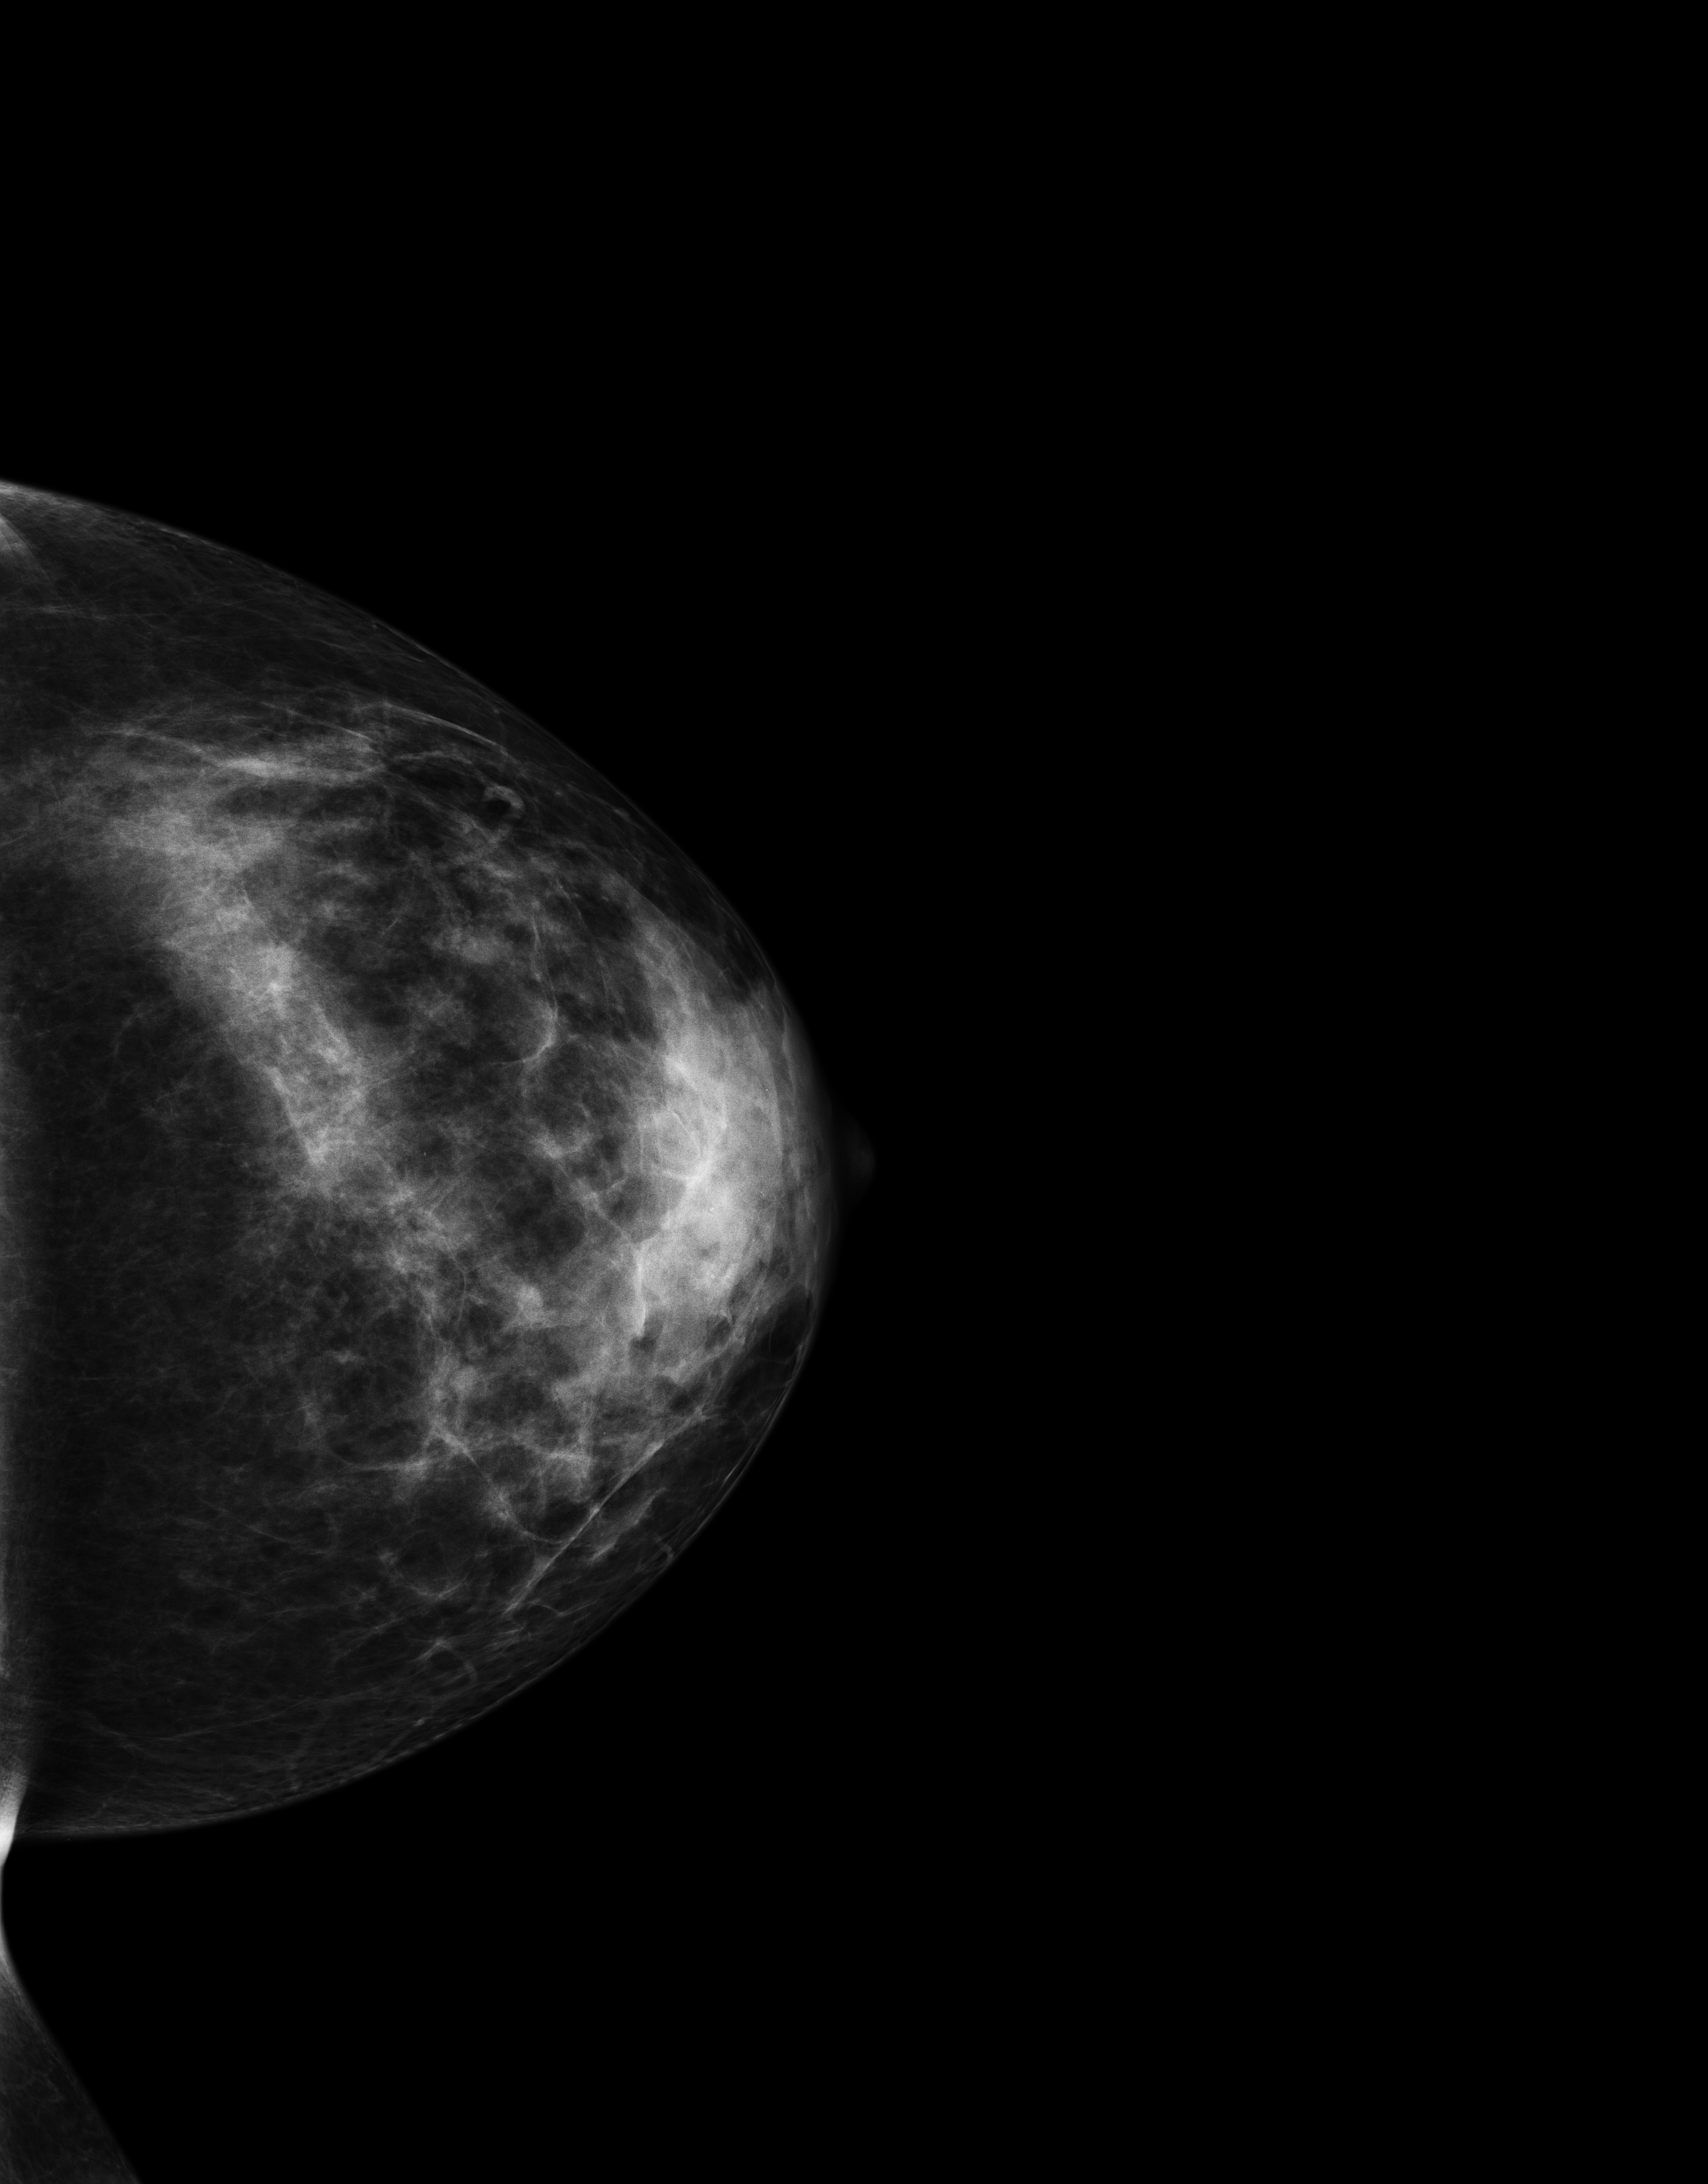
Digital mammogram (FFDM), left breast, CC view, annual screening mammography examination. Patient aged 46 years (female).
- BI-RADS breast density category at the screening exam (both breasts, scale 1–4): 3
- final BI-RADS category for the screening round (tomosynthesis exam, both breasts): category 1
- recall: no recall after this screen